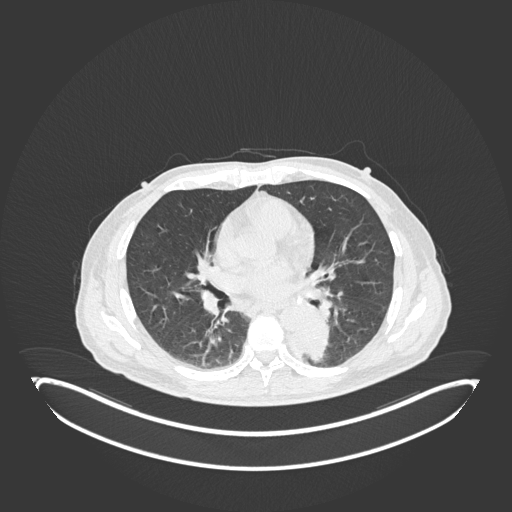
Chest CT, one axial slice; slice 98 of 251 in the series (ordered by position); reconstruction kernel B30f; lung window (W 1500 / L -600 HU); 1 mm slice thickness; 512 × 512 image matrix, field of view 500 × 500 mm. Patient: male, 72 years. From the clinical record (not read from this slice): clinical TNM (as recorded): T2b N0 M1.
Structures marked on this image (bounding box drawn by a radiologist):
- lung tumour (recorded histology: adenocarcinoma): bounding box [x1, y1, x2, y2] px = [284, 315, 330, 363]